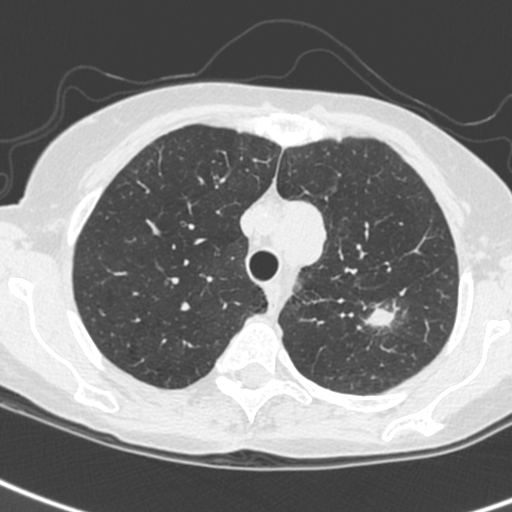
Axial slice from a low-dose chest CT screening exam. First (baseline) screen. Lung window (W 1500 / L -600 HU). 1.3 mm slice thickness. Slice 48 of 242 in the series. 512 × 512 image matrix, field of view 284 × 284 mm. Female participant, aged 61 years at enrolment.
Lesion marked by an expert reader, box from (x=346, y=294) to (x=411, y=348) px. The screening reader recorded 2 non-calcified nodules or masses ≥4 mm on this exam (left upper lobe, left upper lobe); which of them this box marks is not recorded. Official screen result: positive, change unspecified: nodule(s) >= 4 mm or enlarging nodule(s), mass(es), or other non-specific abnormalities suspicious for lung cancer.